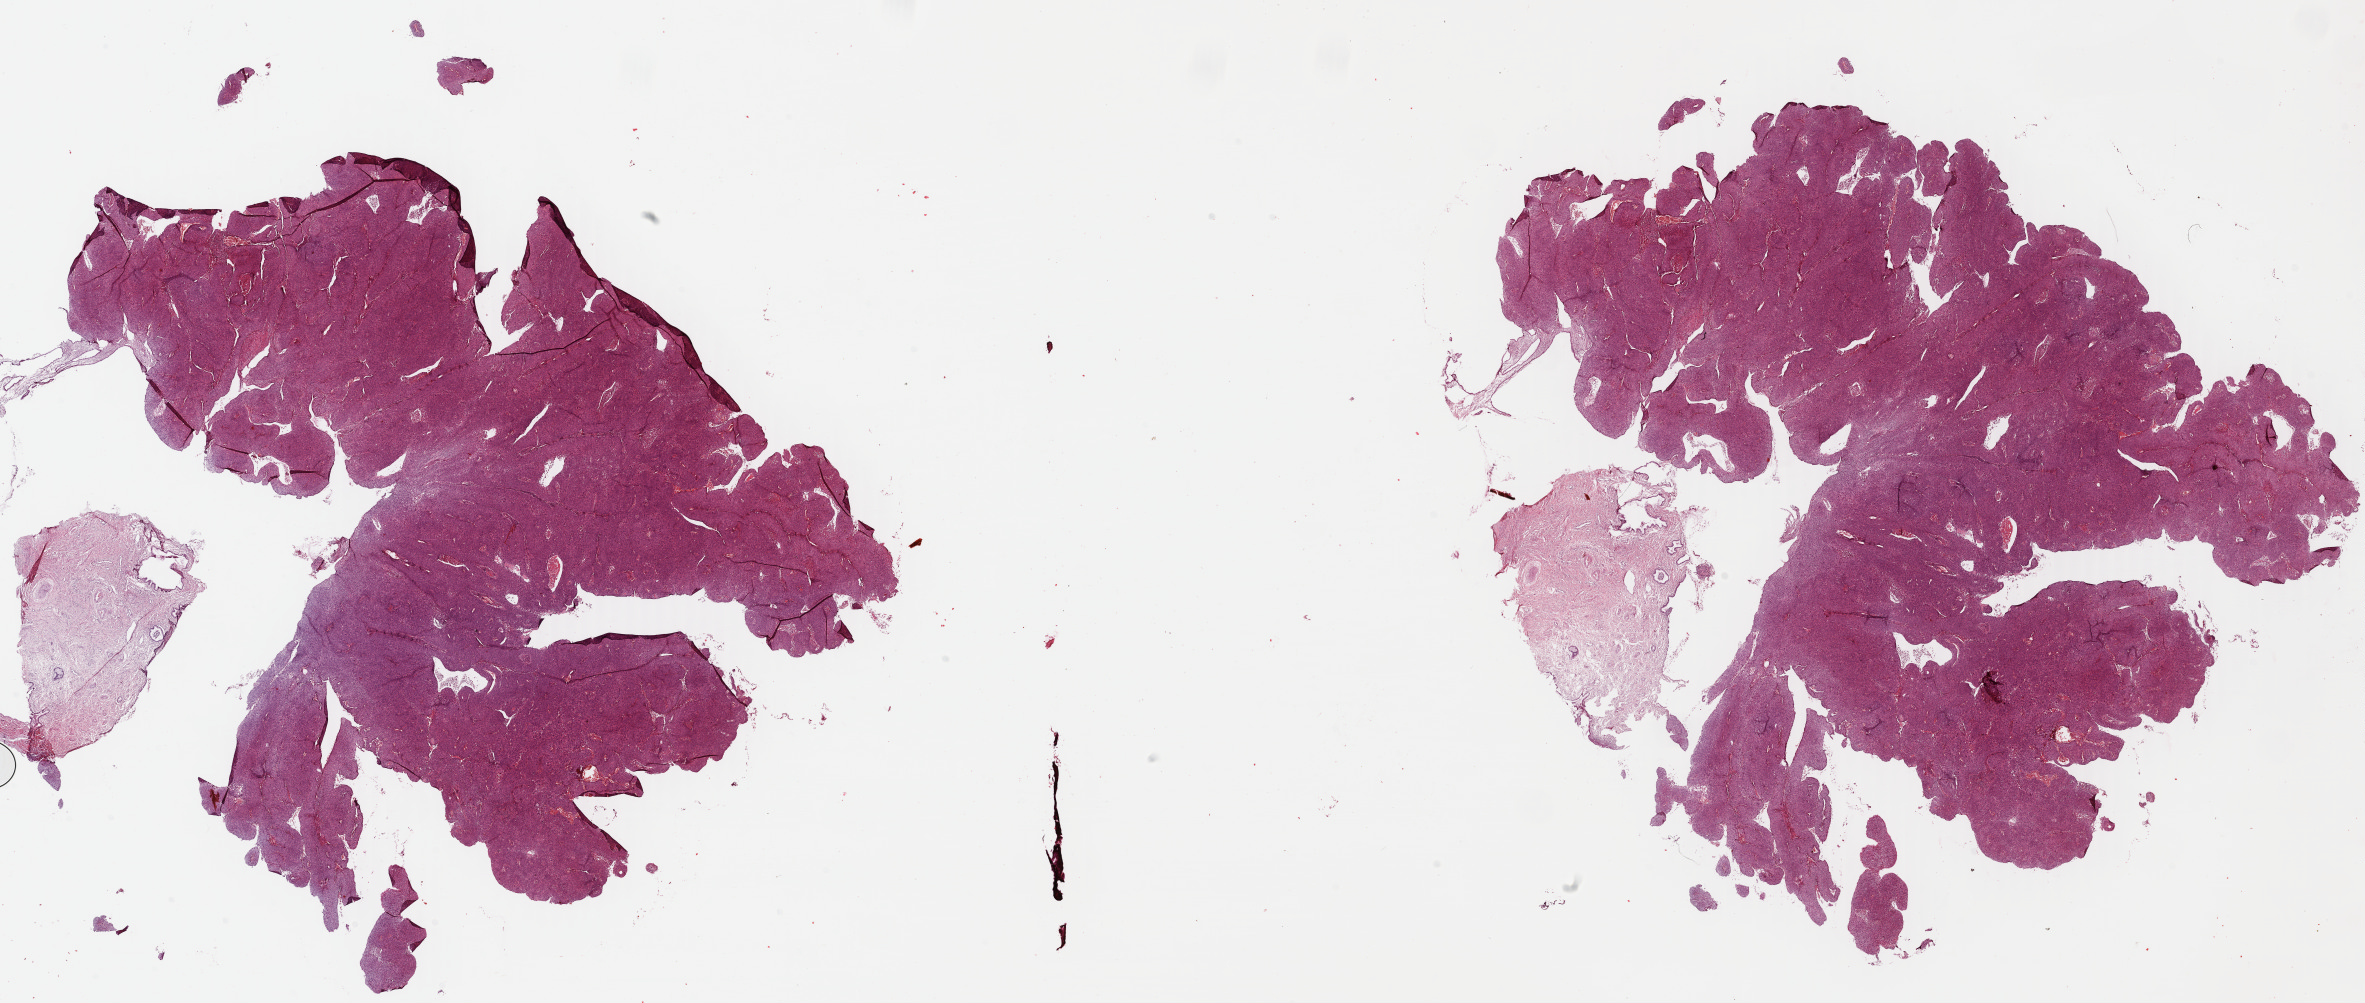
Digitized Hematoxylin and eosin (H&E) stained tissue section (whole slide), a low-resolution overview of the entire scanned area, about 37.2 x 15.8 mm (acquisition: 40x scan); formalin-fixed paraffin-embedded (FFPE) diagnostic section; cervix, primary tumour sample. Female patient; age at initial diagnosis 40 years.
Histologic diagnosis: Squamous cell carcinoma, large cell, nonkeratinizing, NOS (cervix uteri).